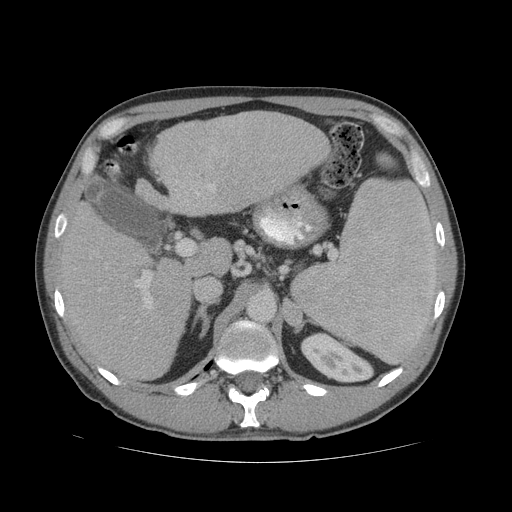
Contrast-enhanced abdominal CT (liver protocol), one axial slice. Slice 37 of 81 in the series (ordered by position). Soft-tissue window (W 400 / L 40 HU). 2.5 mm slice thickness. 512 × 512 image matrix, field of view 400 × 400 mm. Case-level facts recorded for this patient, not image findings: diagnosis: hepatocellular carcinoma (patient treated with transarterial chemoembolisation; whether this scan precedes or follows treatment is not stated here); TNM stage (as recorded): Stage-IVB; Child-Pugh class: B; tumour differentiation: well differentiated; tumour nodularity: multinodular.
Annotated regions visible in this slice (semi-automatic segmentation, software-assisted and operator-edited):
- liver parenchyma outside the tumour (the mass and vessels are separate outlines, so this box may not span the whole liver): bounding box (x1, y1, x2, y2) in pixels: (57, 110, 330, 380)
- liver vessels: (60, 148, 215, 309)